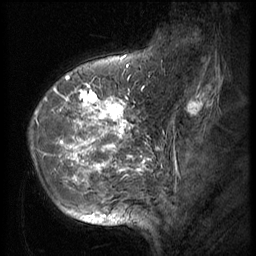
Breast MRI (dynamic contrast-enhanced), one sagittal slice; position 16 of 56 along the scan axis; 3 images stored at this slice position (order not interpretable as contrast timing); 1.5 T; TE 4.2 ms, TR 9 ms; 2.5 mm slice thickness; 256 × 256 image matrix, field of view 180 × 180 mm. Patient: female, 49 years. From the clinical record (not read from this slice): setting: breast cancer imaged before/during neoadjuvant chemotherapy; receptor status: HER2-positive.
Annotated regions visible in this slice (semi-automatically segmented with operator editing):
- analysis volume of interest (the breast-tissue region the enhancement analysis was run in; not a lesion): bounding box (x1, y1, x2, y2) in pixels: (28, 79, 142, 203)
- tumour enhancement mask (voxels above the 140 % enhancement threshold inside the analysis volume of interest): (36, 79, 141, 188)